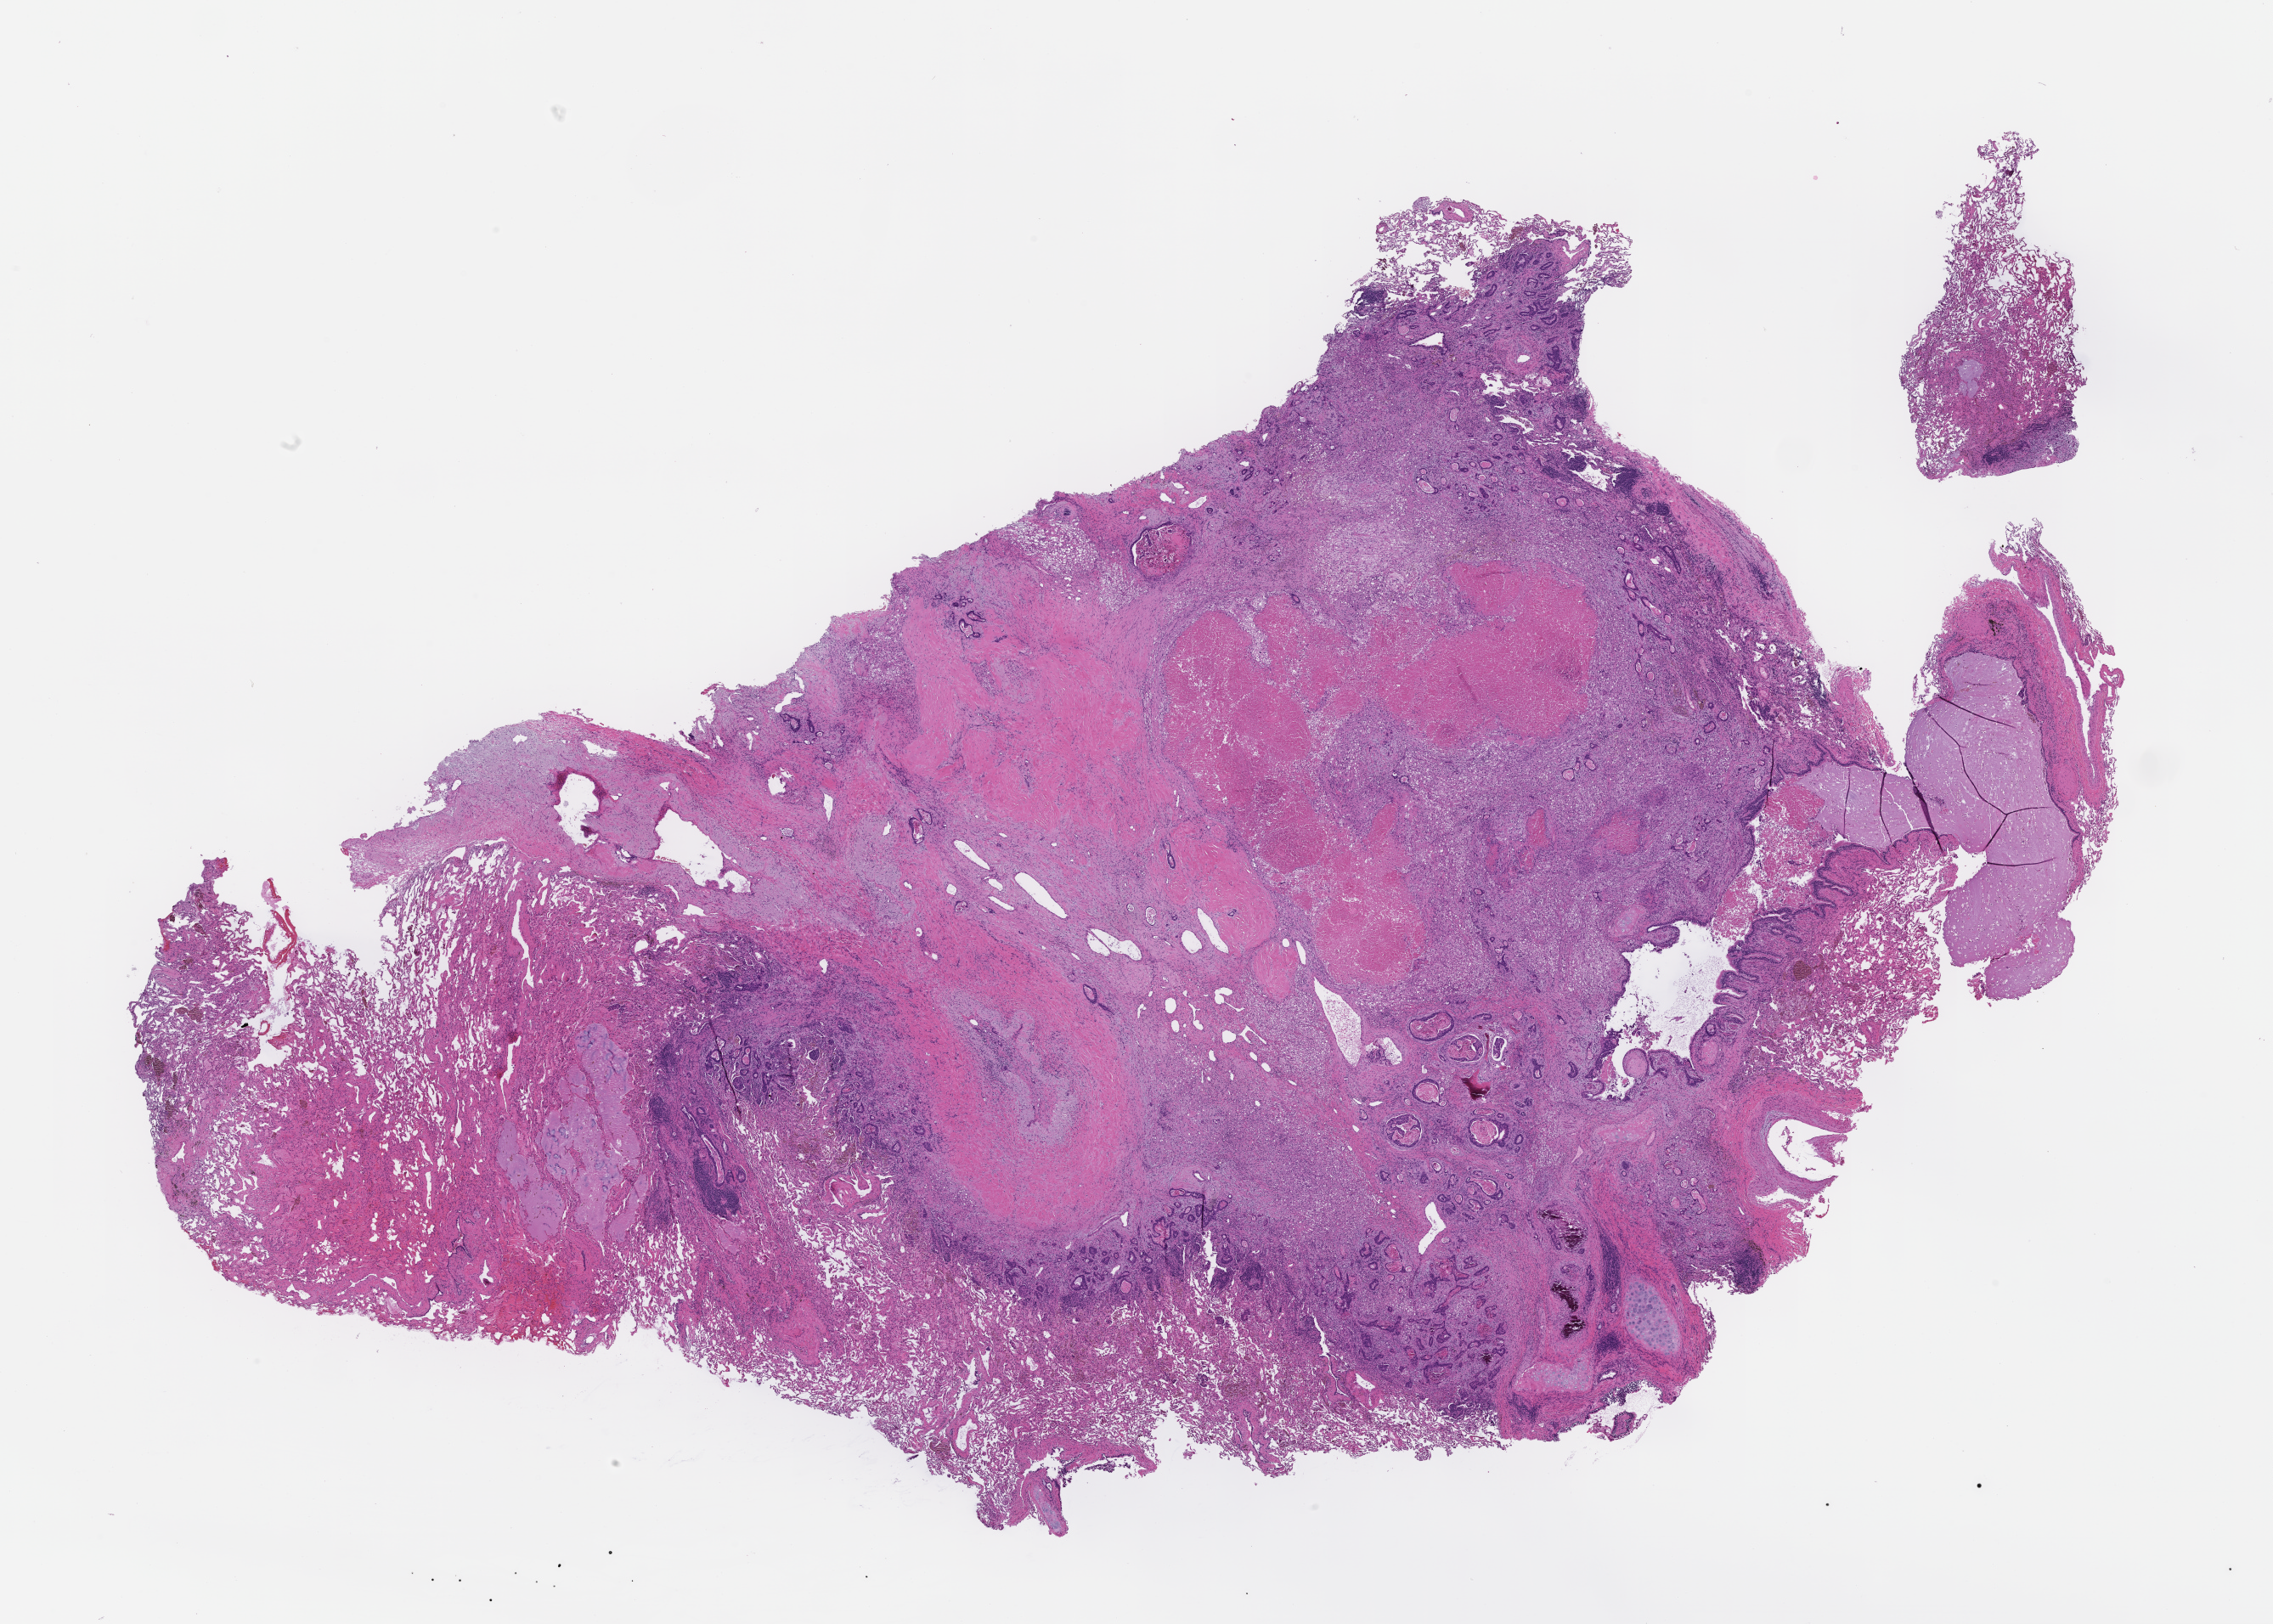
Digitized H&E-stained section — a low-resolution overview of the entire scanned area, about 21.6 x 15.4 mm, FFPE section, collected on treatment. Patient: male.
This section: metastatic tumor tissue. Primary diagnosis of the patient: Colorectal Carcinoma.